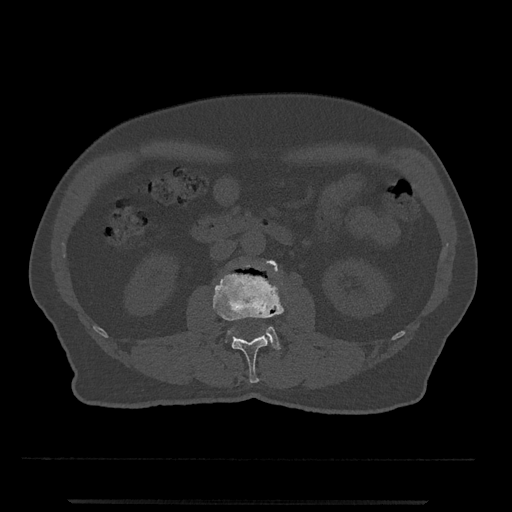
CT including the spine, one axial slice; slice 246 of 797 in the series (ordered by position); reconstruction kernel Br40s/3; bone window (W 1800 / L 400 HU); 512 × 512 image matrix. Patient: male, 63 years. Case-level facts recorded for this patient, not image findings: primary cancer: prostate.
Structures marked on this image (semi-automatic segmentation, software-assisted and operator-edited):
- L2 vertebra: box from (x=213, y=263) to (x=283, y=383) px
- L3 vertebra: (x=228, y=260)–(x=280, y=350)